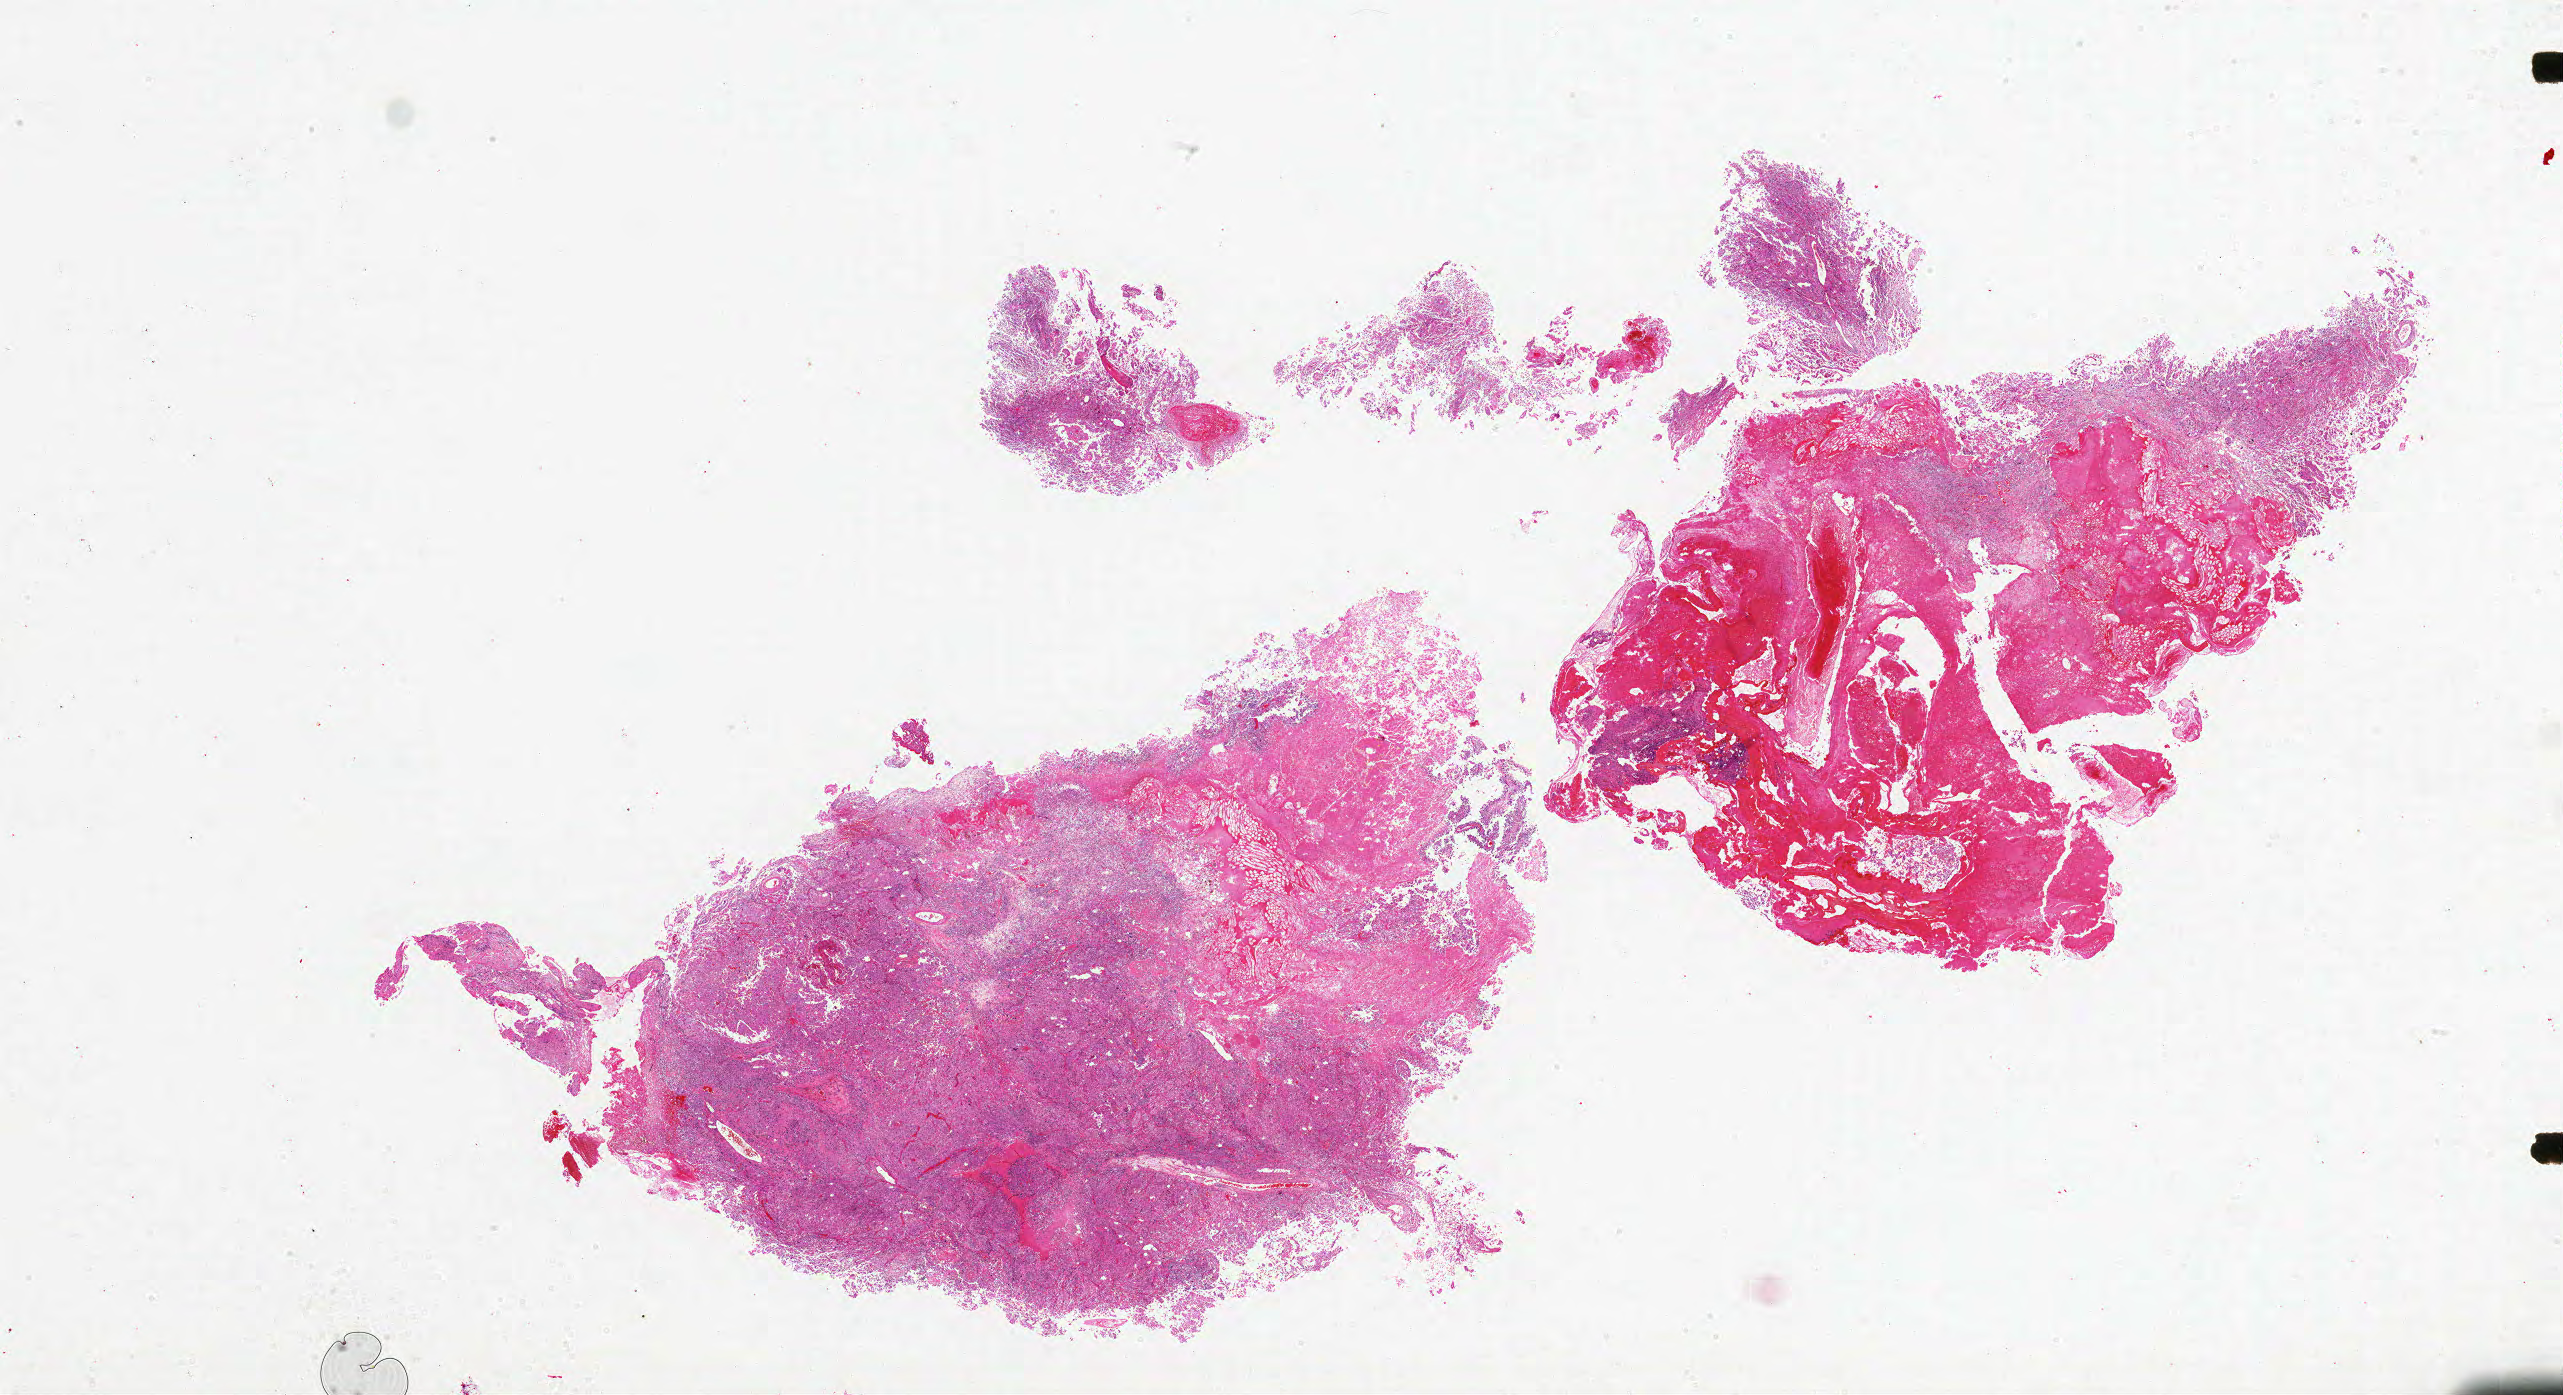
Digitized H&E tissue section (whole slide) — low-resolution overview of the scanned area, about 41.0 x 22.3 mm, formalin-fixed paraffin-embedded (FFPE) diagnostic section, sample: primary tumour, brain. Patient: male, age at initial diagnosis 58 years.
* diagnosis: Glioblastoma